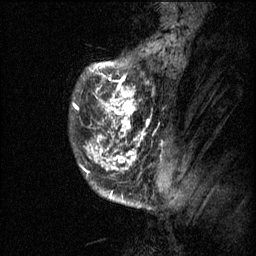
Breast MRI (dynamic contrast-enhanced), one sagittal slice. Position 11 of 60 along the scan axis. 3 images stored at this slice position (order not interpretable as contrast timing). 1.5 T. TE 4.2 ms, TR 11.1 ms. 2 mm slice thickness. 256 × 256 image matrix, field of view 180 × 180 mm. Patient: female, 50 years.
Outlined on this slice (semi-automatic segmentation, software-assisted and operator-edited):
- analysis volume of interest (the breast-tissue region the enhancement analysis was run in; not a lesion): bounding box (x1, y1, x2, y2) in pixels: (70, 68, 153, 141)
- tumour enhancement mask (voxels above the 70 % enhancement threshold inside the analysis volume of interest): (74, 68, 149, 141)